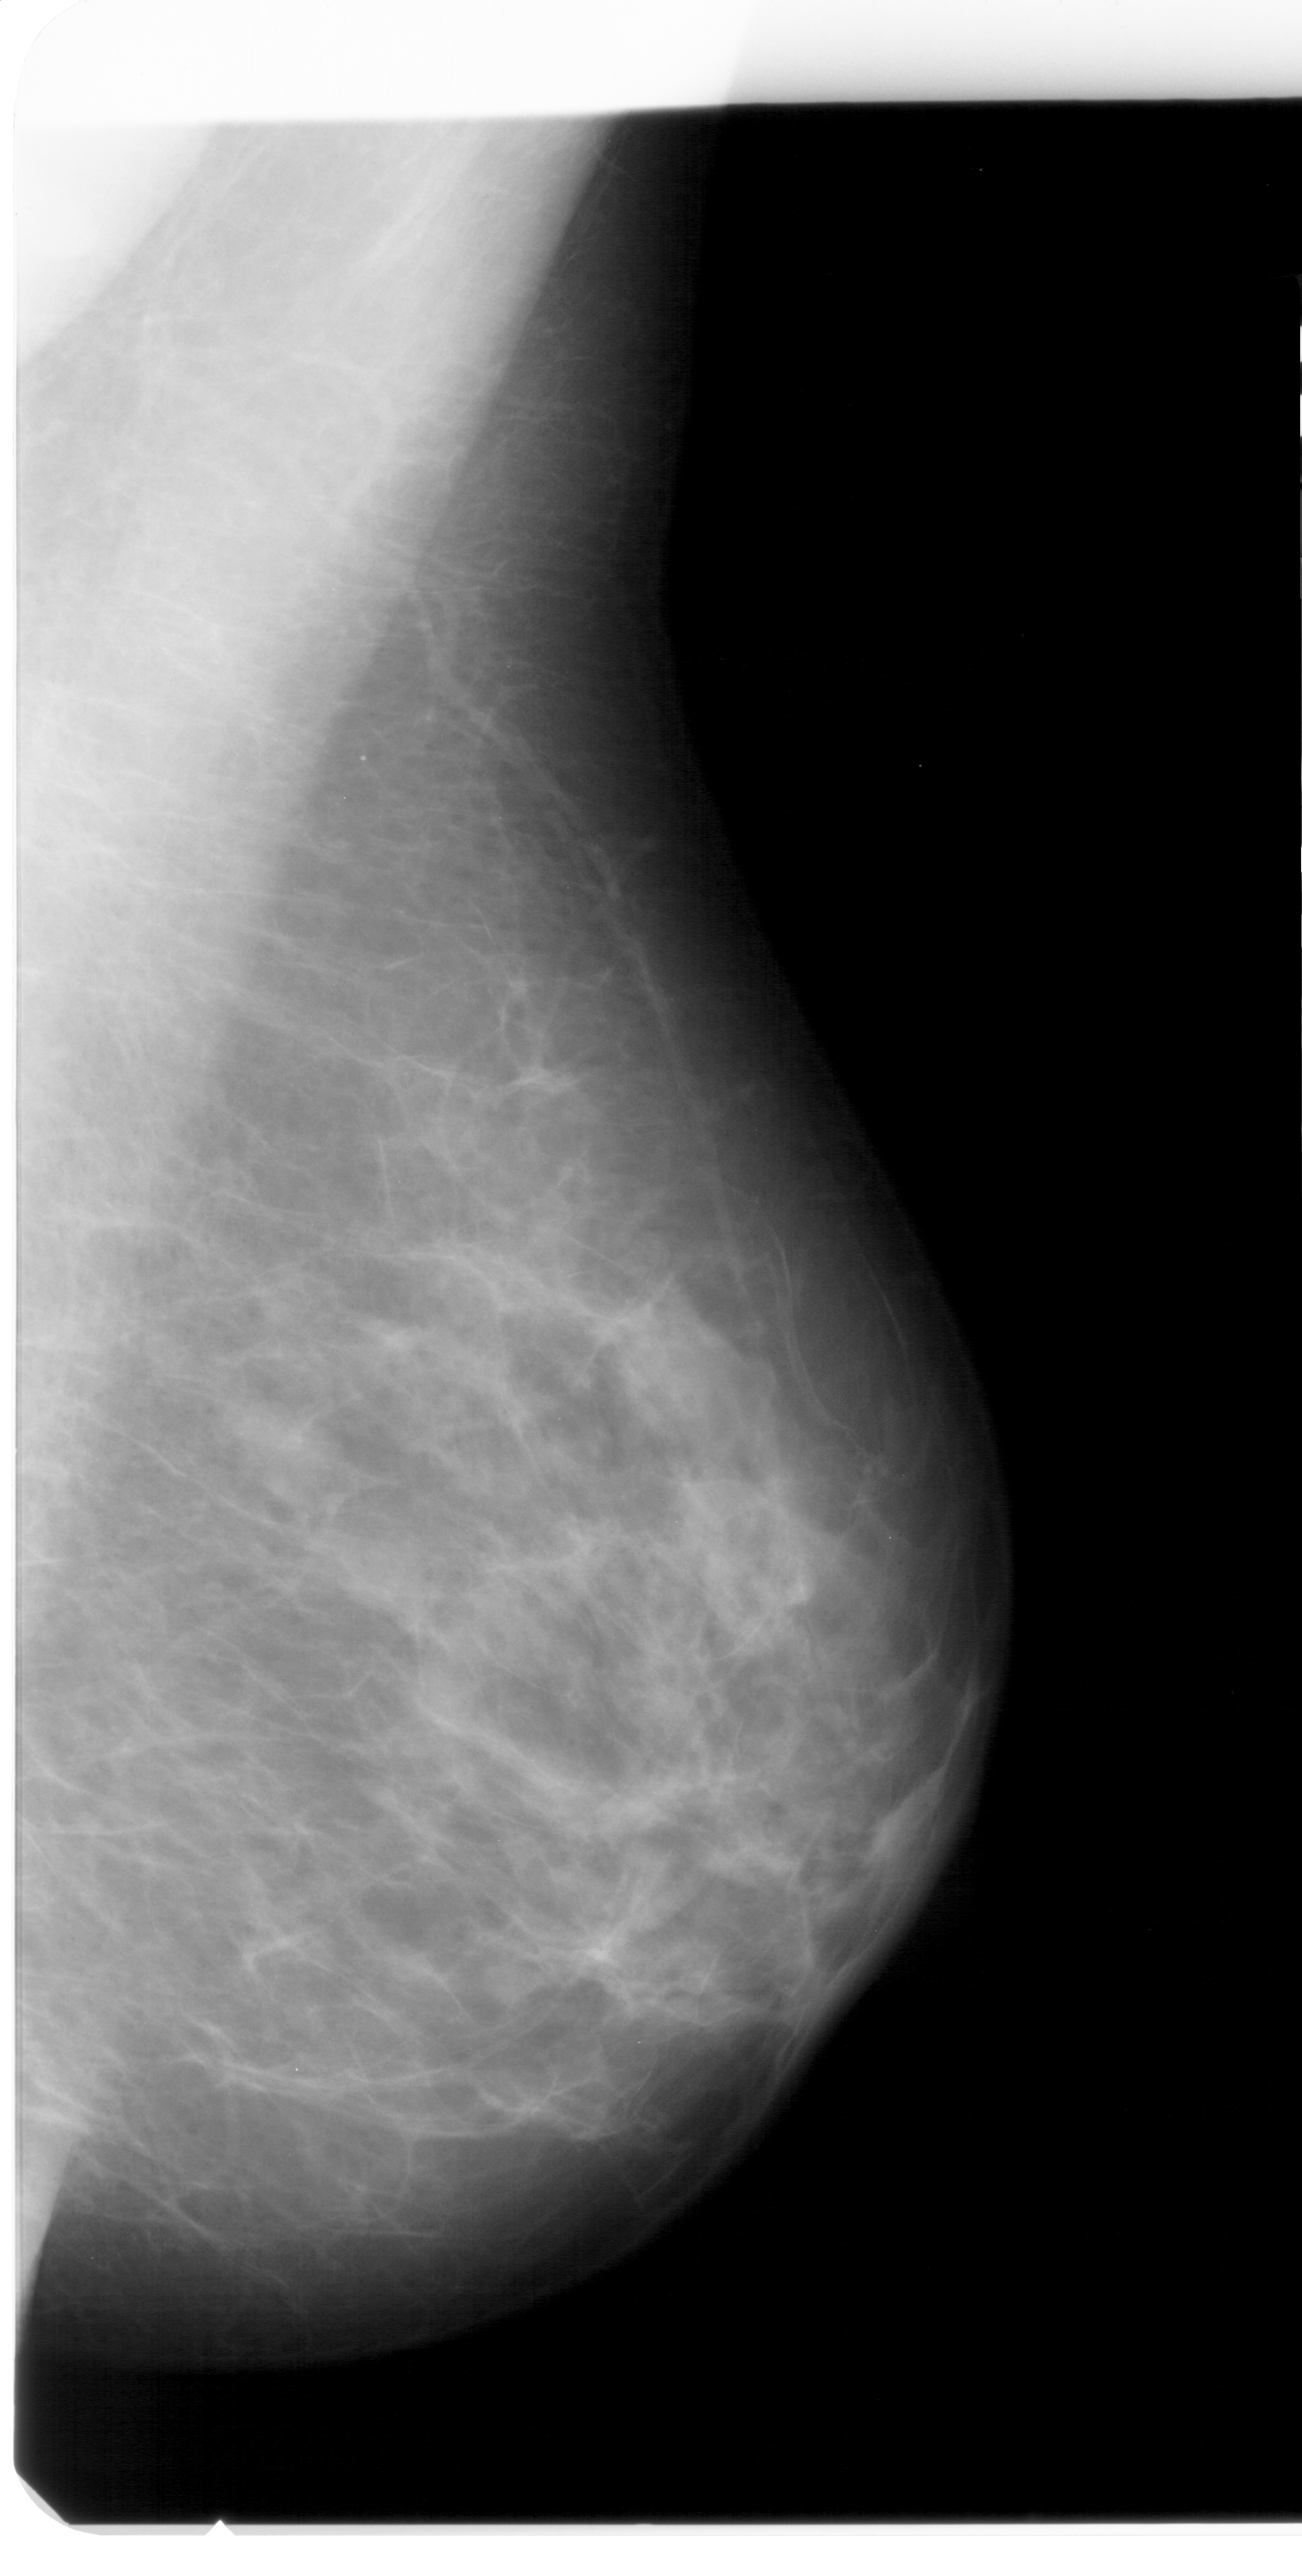
Digitized screen-film mammogram, right breast, MLO view, breast composition: scattered fibroglandular densities (BI-RADS density category 2 of 4).
Abnormality record for this image: mass, shape oval, margins ill defined; BI-RADS assessment category 4; subtlety rating 4 on a 1 (subtle) to 5 (obvious) scale; pathology result (as recorded, not read from the image): benign.